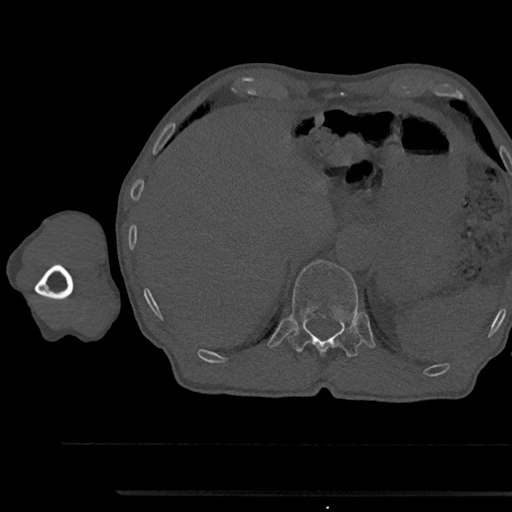
CT including the spine, one axial slice. Slice 720 of 797 in the series (ordered by position). Bone window (W 1800 / L 400 HU). 0.5 mm slice thickness. 512 × 512 image matrix, field of view 367 × 367 mm. Male patient, age 79 years. From the clinical record (not read from this slice): primary cancer: prostate.
Outlined on this slice (semi-automatic segmentation, software-assisted and operator-edited):
- T12 vertebra: box from (x=289, y=260) to (x=362, y=357) px